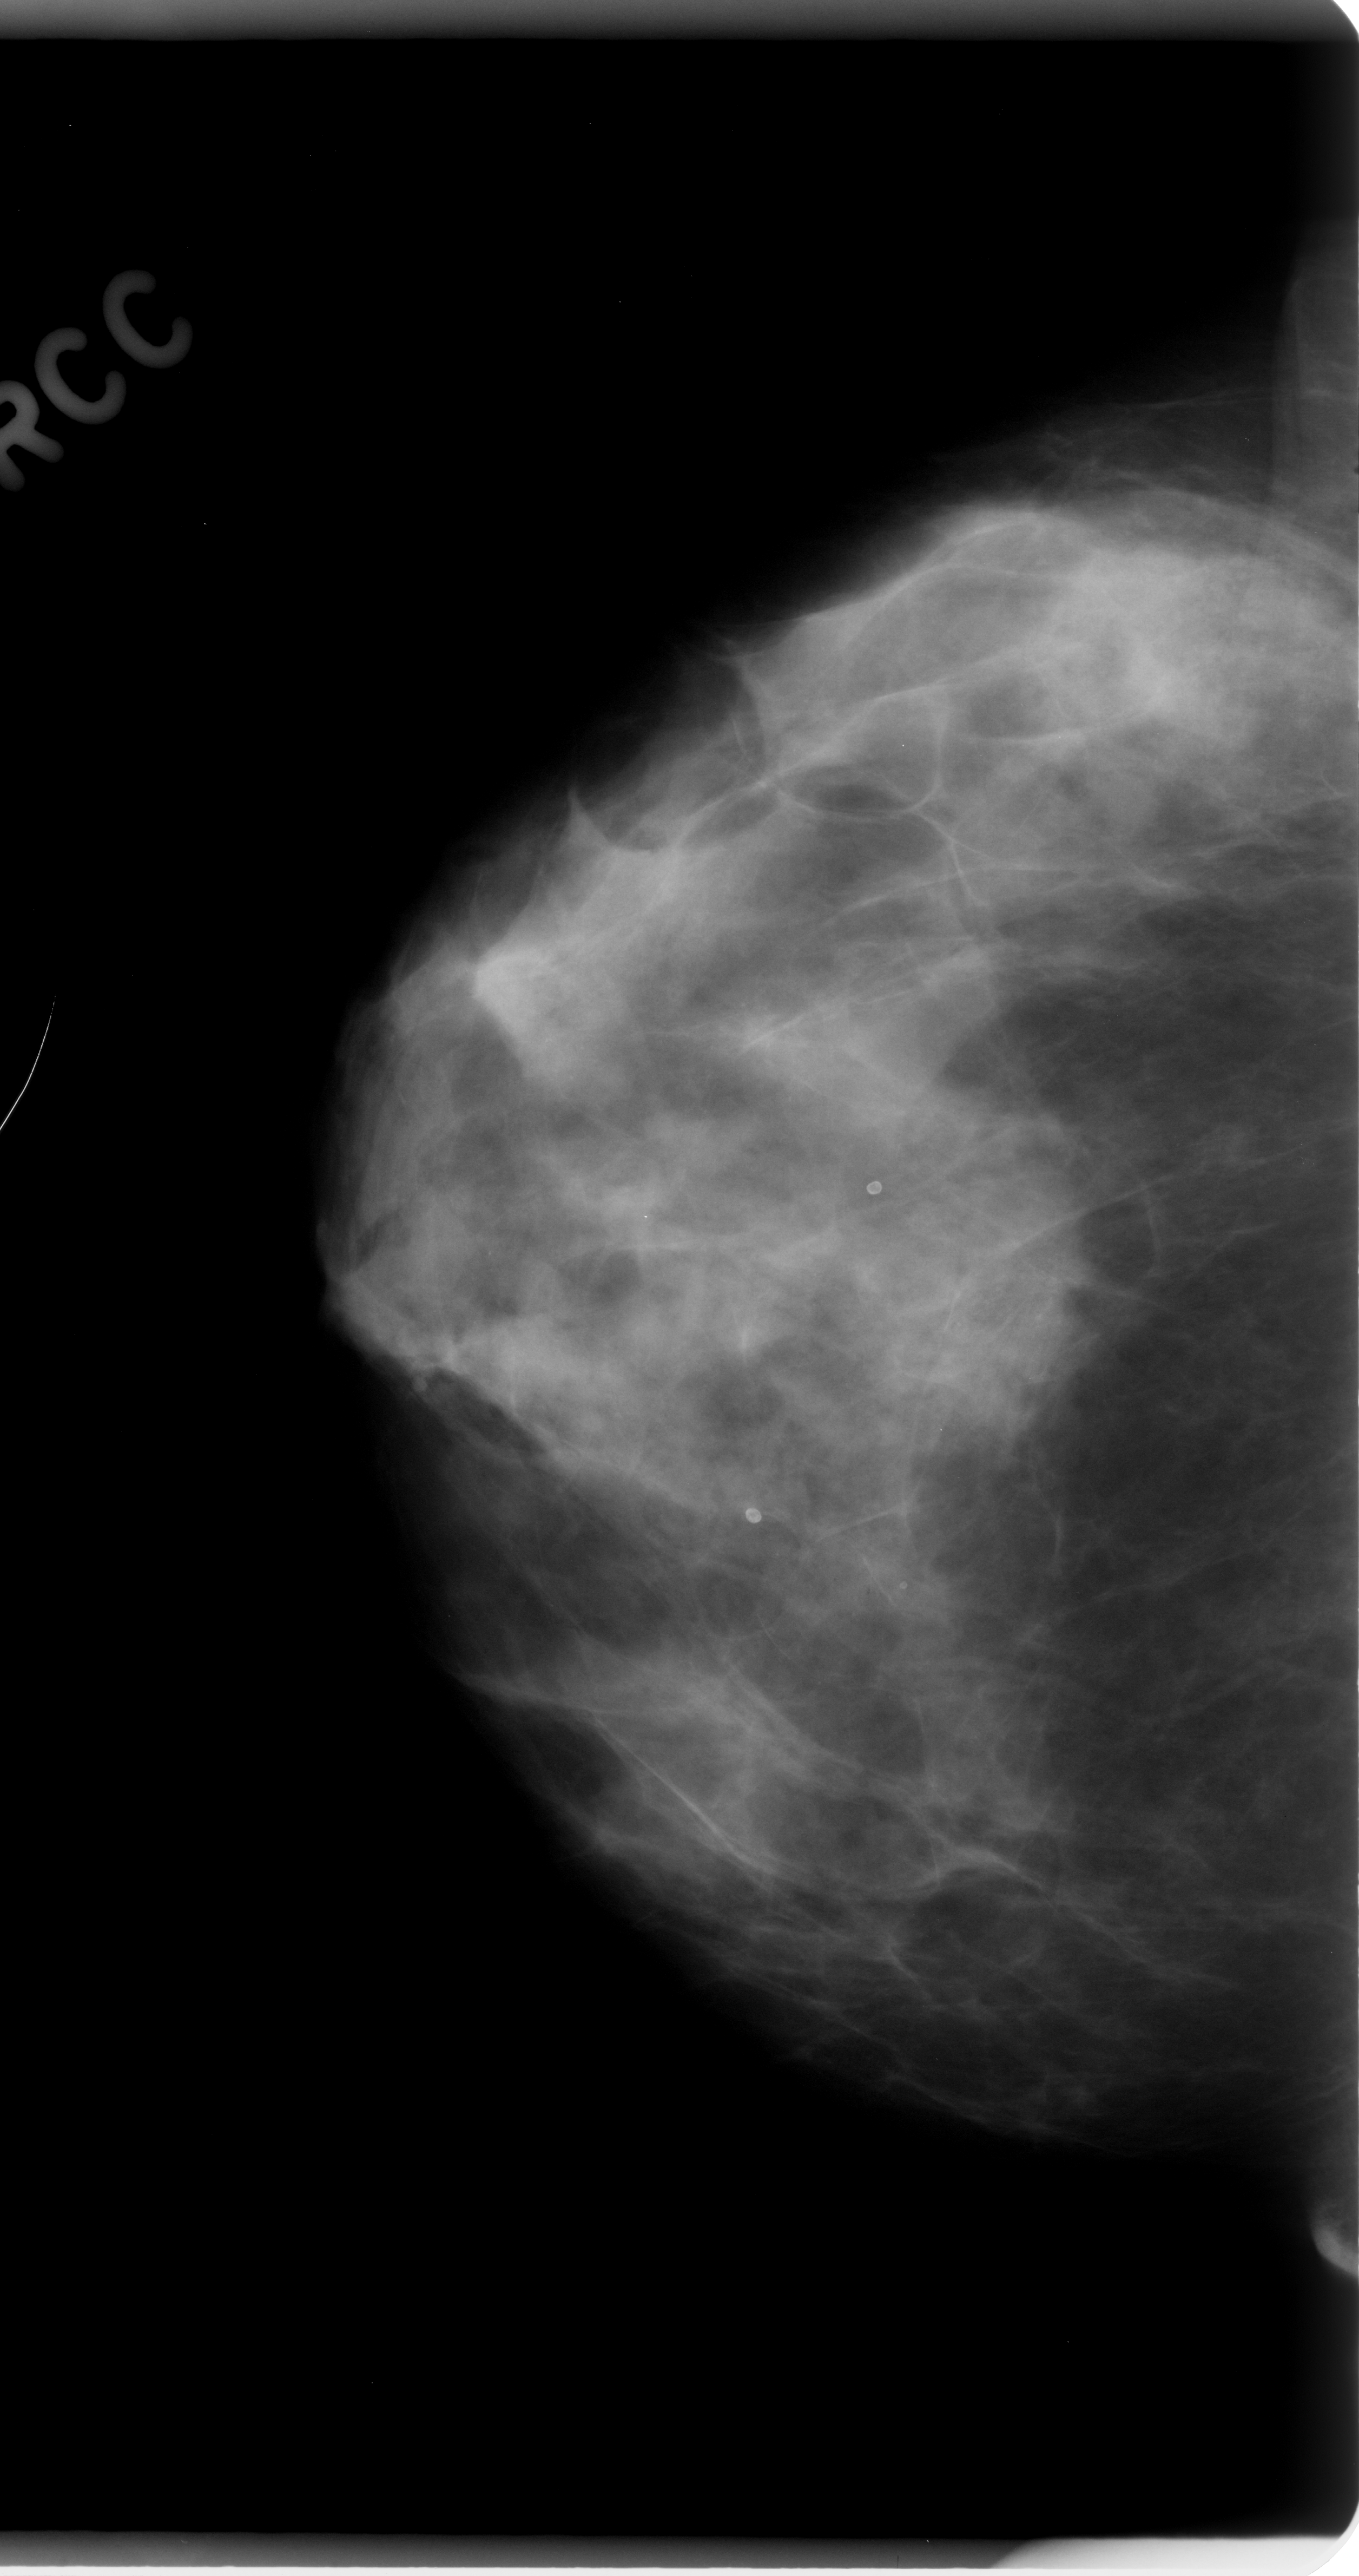
Digitized screen-film mammogram. Right breast. CC view. BI-RADS breast density category 3 (scale 1–4). 1359 × 2576 image matrix.
Expert-marked regions of interest on this film, with their recorded descriptors:
- calcifications, morphology amorphous, distribution clustered; BI-RADS assessment category 5; subtlety rating 5 on a 1 (subtle) to 5 (obvious) scale; pathology (as recorded): malignant: bounding box (x1, y1, x2, y2) in pixels: (783, 1065, 1131, 1508)